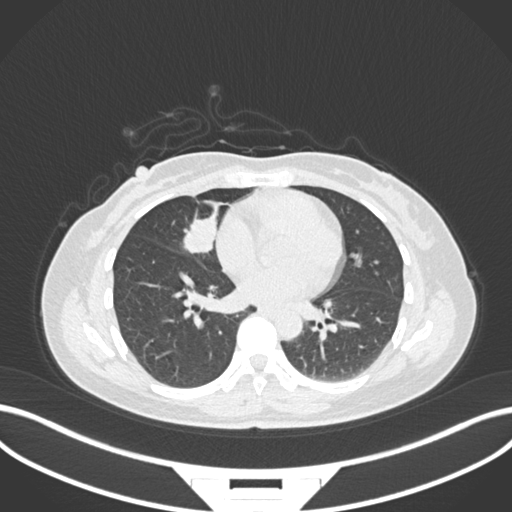
Chest CT, one axial slice. Position 69 of 171 along the scan axis. Reconstruction kernel B30f. 120 kVp. Lung window (W 1500 / L -600 HU). 1 mm slice thickness. 512 × 512 image matrix. Female patient, age 43 years. From the clinical record (not read from this slice): clinical TNM (as recorded): T1c N3 M1.
Structures marked on this image (rectangle marked by the reading radiologist):
- lung tumour (recorded histology: adenocarcinoma): bounding box <180,212,220,257> (left, top, right, bottom; pixels)